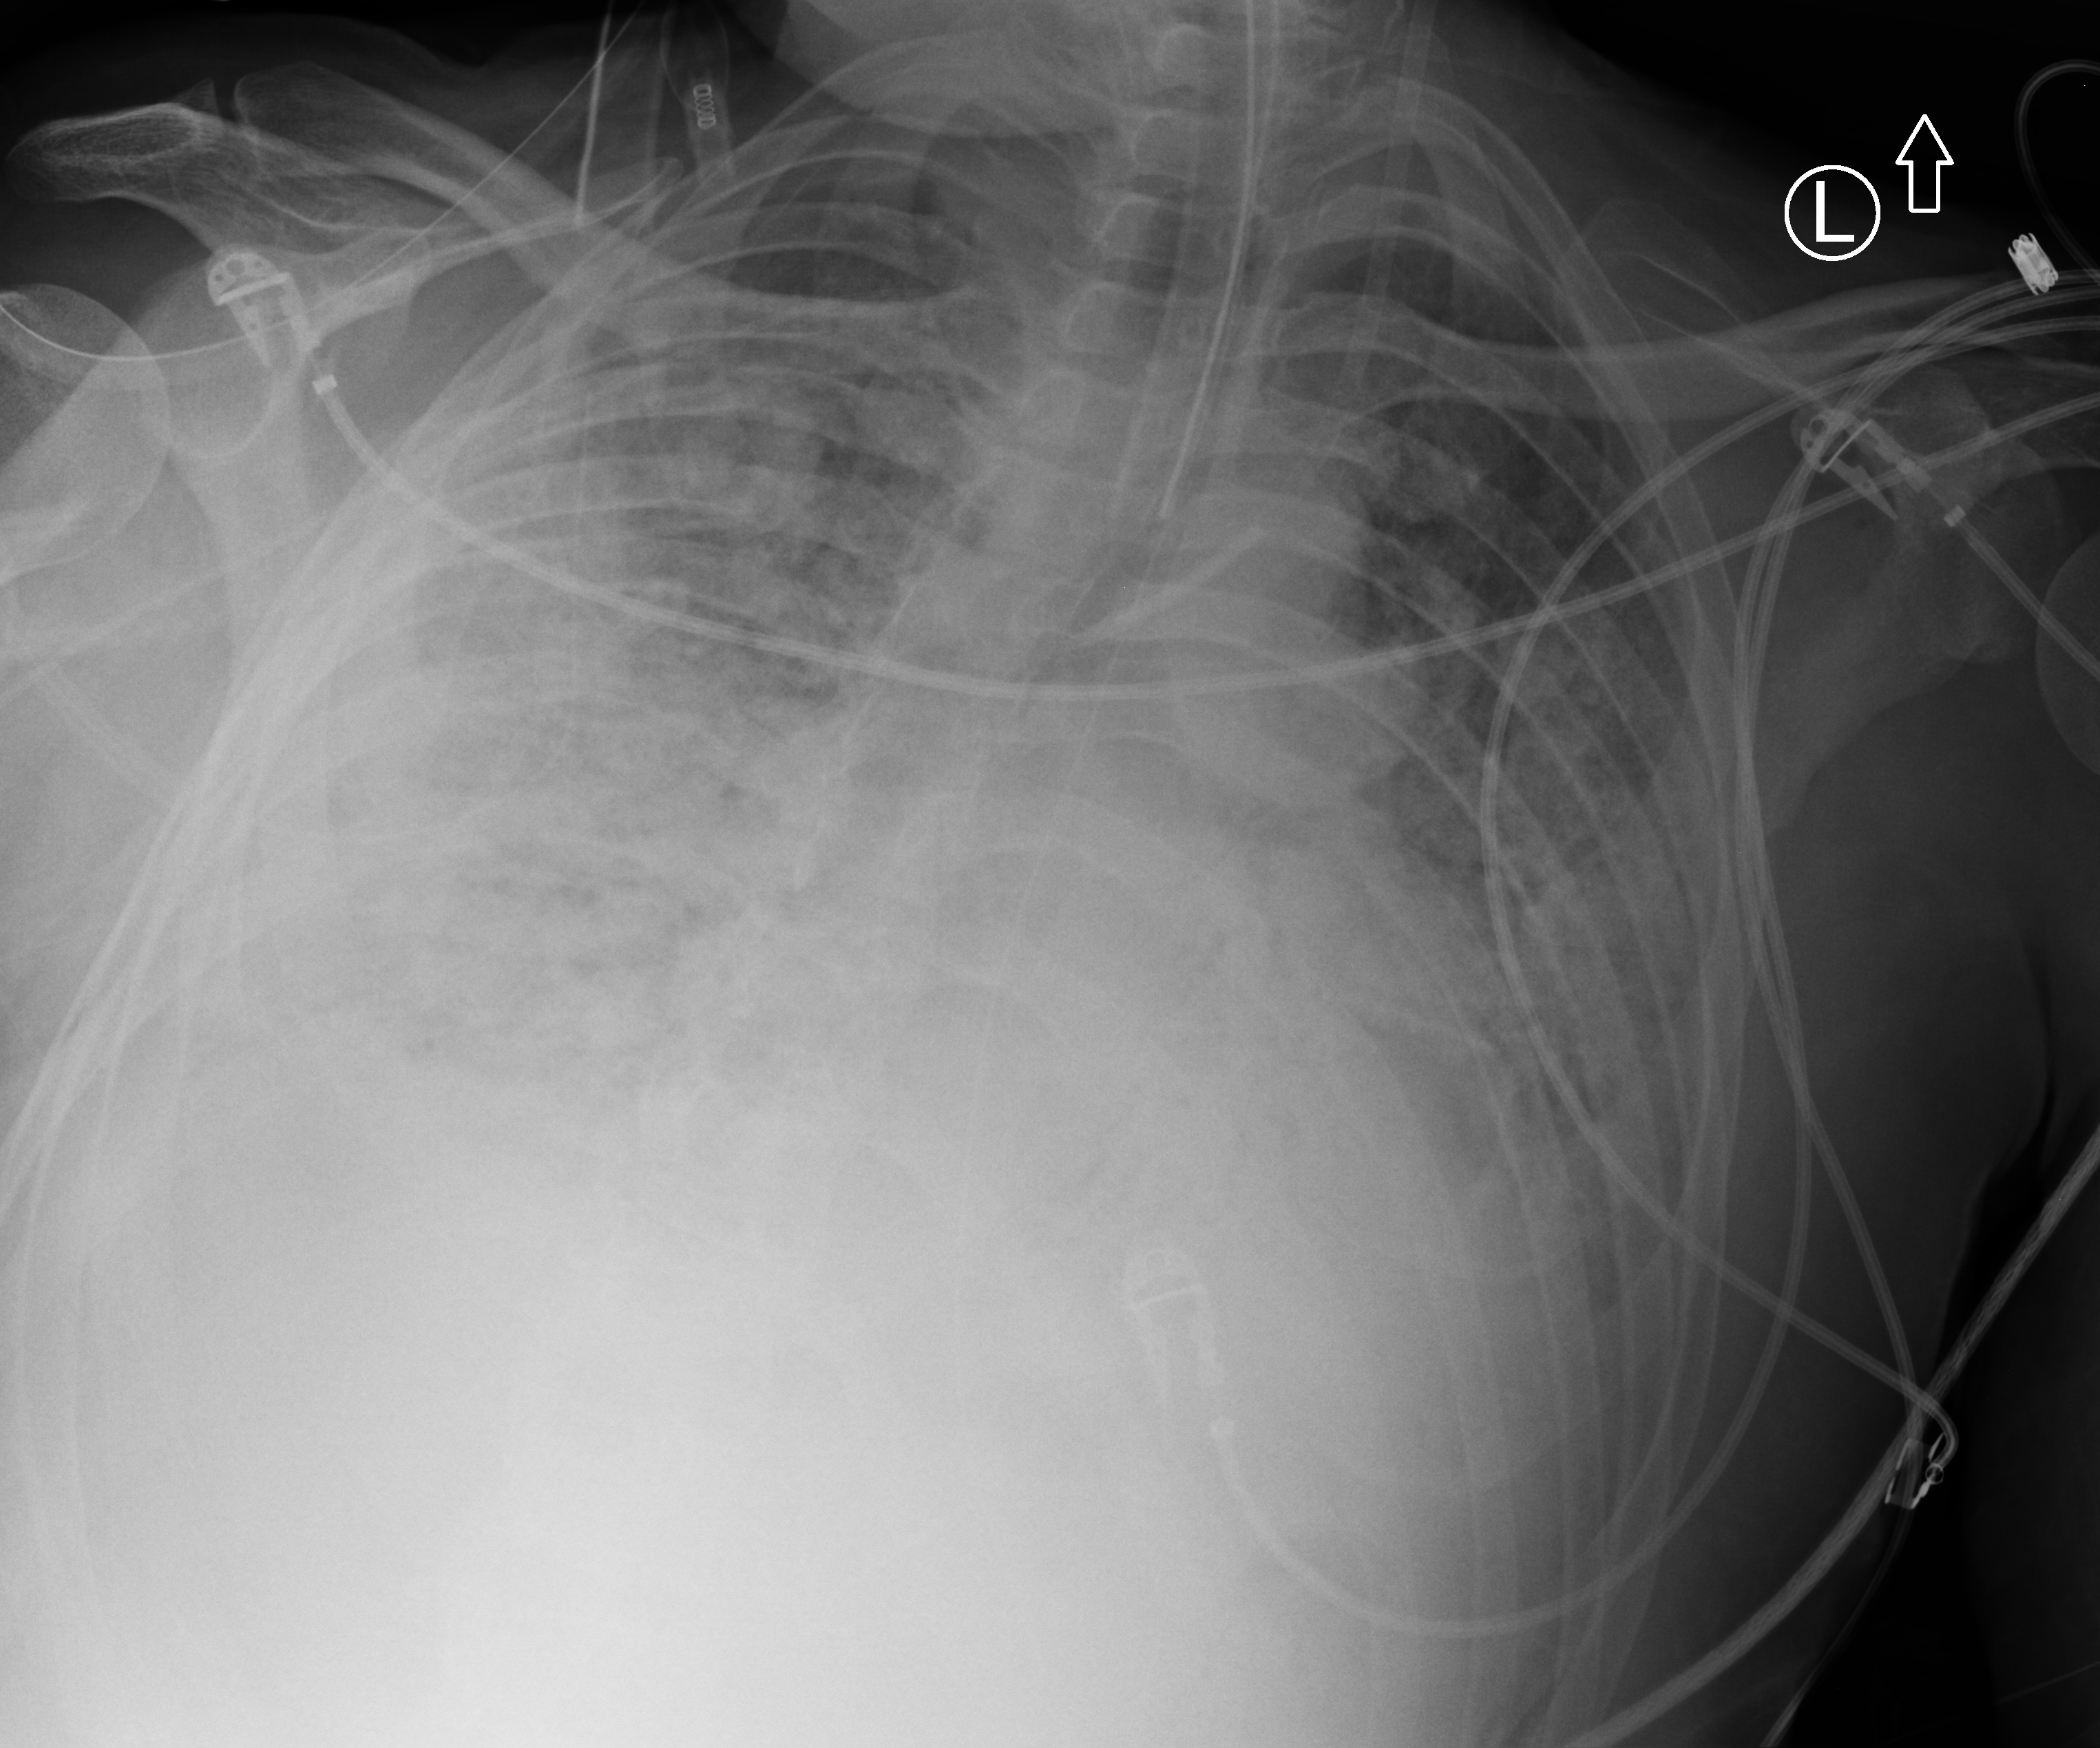
Chest X-ray (portable); anteroposterior (AP) projection. Patient hospitalised with COVID-19; male, aged 18–59 years.
From the hospital-stay record, not from the radiograph (when in the stay this image was taken is not recorded): other chronic lung disease (admission record): no; admitted to intensive care during this hospital stay: yes; COPD (admission record): no.